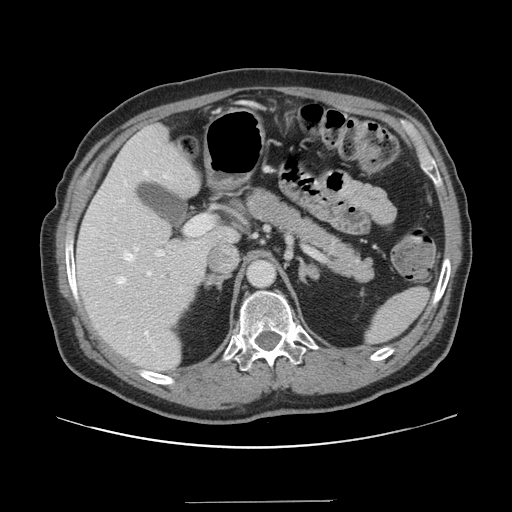
Contrast-enhanced abdominal CT, one axial slice. Position 92 of 151 along the scan axis. Intravenous contrast given. Soft-tissue window (W 400 / L 40 HU). 2.5 mm slice thickness. 512 × 512 image matrix, field of view 399 × 399 mm. Male patient, age 63 years. Case-level facts recorded for this patient, not image findings: diagnosis: colorectal cancer liver metastases, imaged before liver resection; multiple liver metastases: no; largest metastasis: 2.1 cm; disease in both lobes: no.
Outlined on this slice (manually delineated by an expert):
- hepatic veins: bounding box <117,170,156,351> (left, top, right, bottom; pixels)
- liver: <77,125,237,373>
- planned liver remnant (the part of the liver to remain after resection): <76,125,237,372>
- portal vein (with intrahepatic branches): <155,215,212,257>